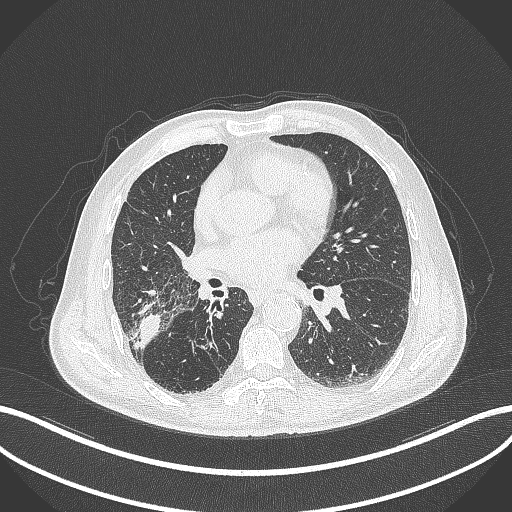
Chest CT, one axial slice. 120 kVp. Lung window (W 1500 / L -600 HU). 512 × 512 image matrix, field of view 400 × 400 mm. Male patient, age 72 years. Case-level facts recorded for this patient, not image findings: clinical TNM (as recorded): T3 N2 M0.
Annotated regions visible in this slice (rectangle marked by the reading radiologist):
- lung tumour (recorded histology: adenocarcinoma): bounding box <129,310,165,354> (left, top, right, bottom; pixels)